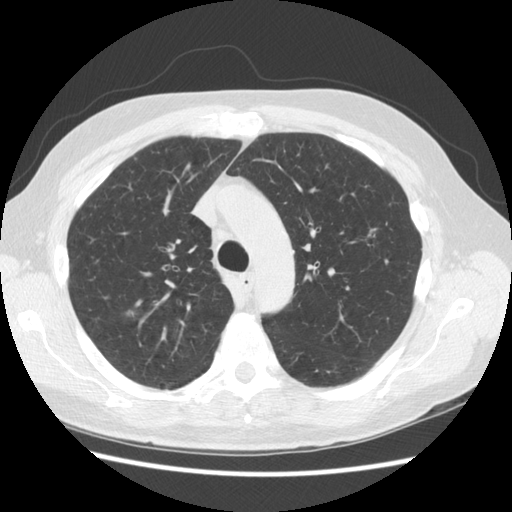
Low-dose screening chest CT, one axial slice; slice 113 of 156 in the series (ordered by position); lung window (W 1500 / L -600 HU); 512 × 512 image matrix.
Outlined on this slice (outlined manually by an expert reader):
- lesion 1 (tumor, upper lobe of right lung): bounding box (x1, y1, x2, y2) in pixels: (123, 307, 137, 320)